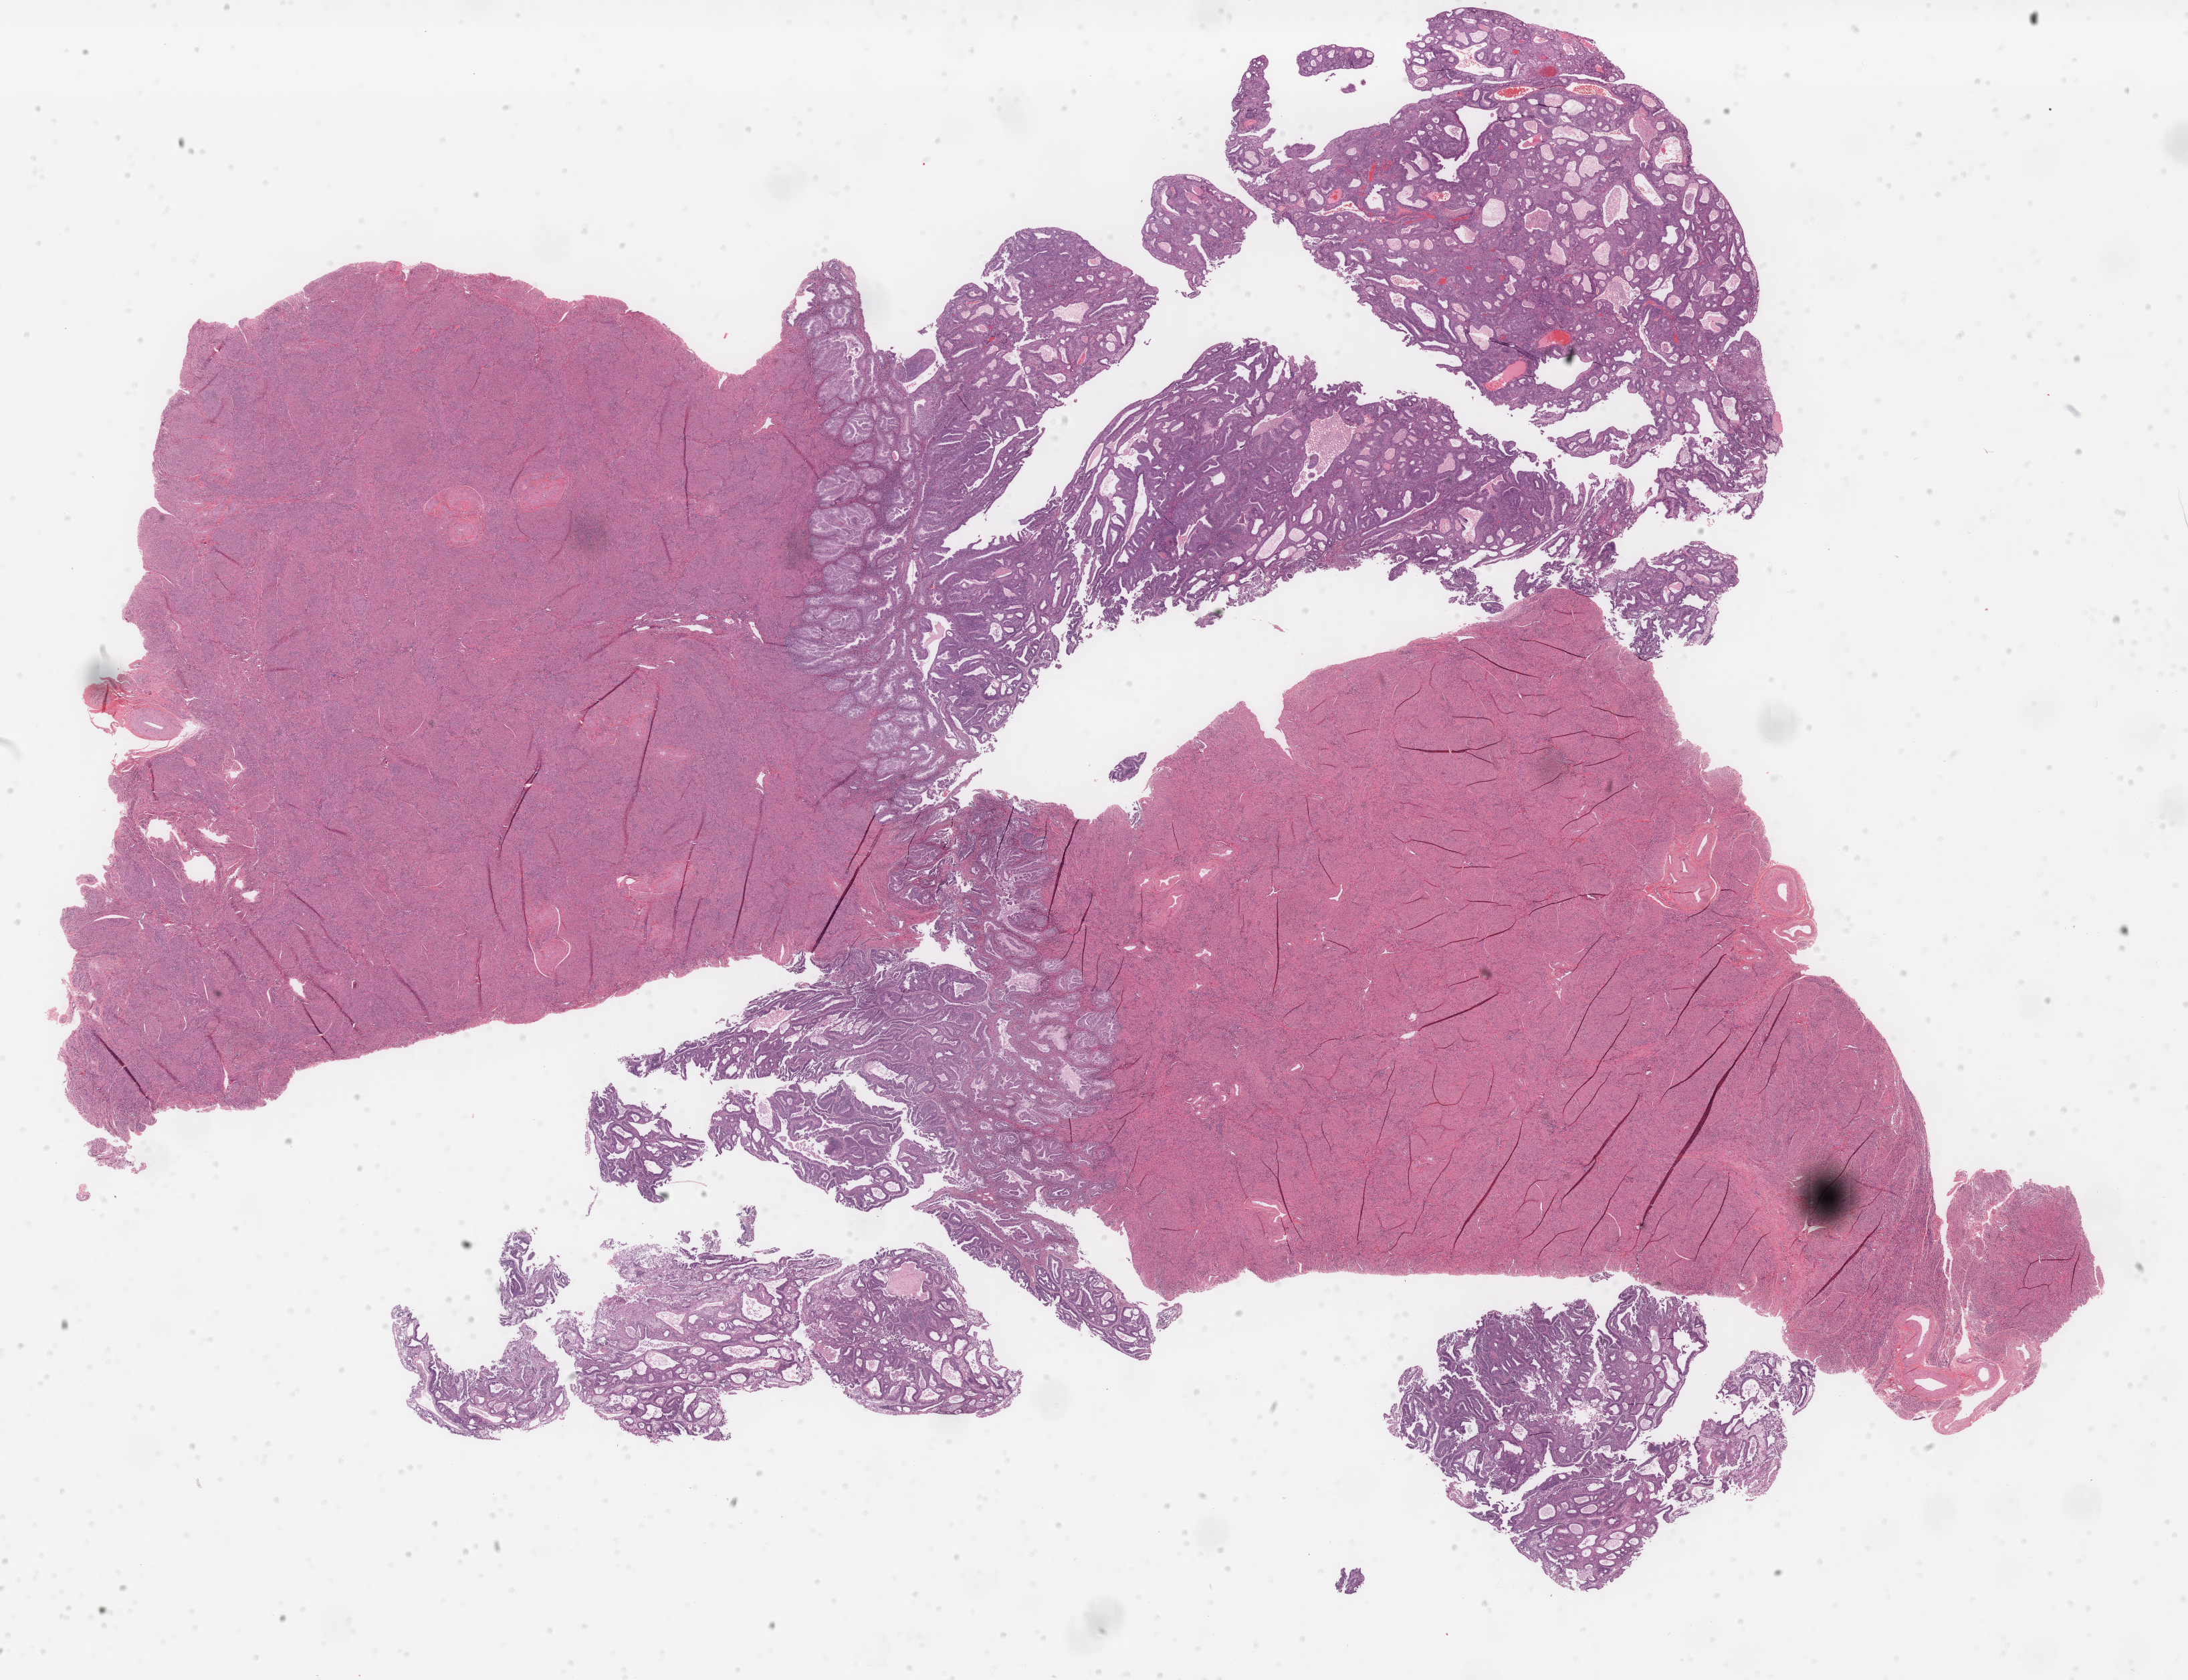
H&E-stained whole-slide image — a low-resolution overview of the entire scanned area, about 26.0 x 19.9 mm (from a 40x scan). Formalin-fixed paraffin-embedded (FFPE) diagnostic section. Sample: primary tumour, uterus. Patient: female, age at initial diagnosis 61 years. Histologic grade: G1 (well differentiated).
FIGO stage: IA. Diagnosis: Endometrioid adenocarcinoma, NOS (endometrium).